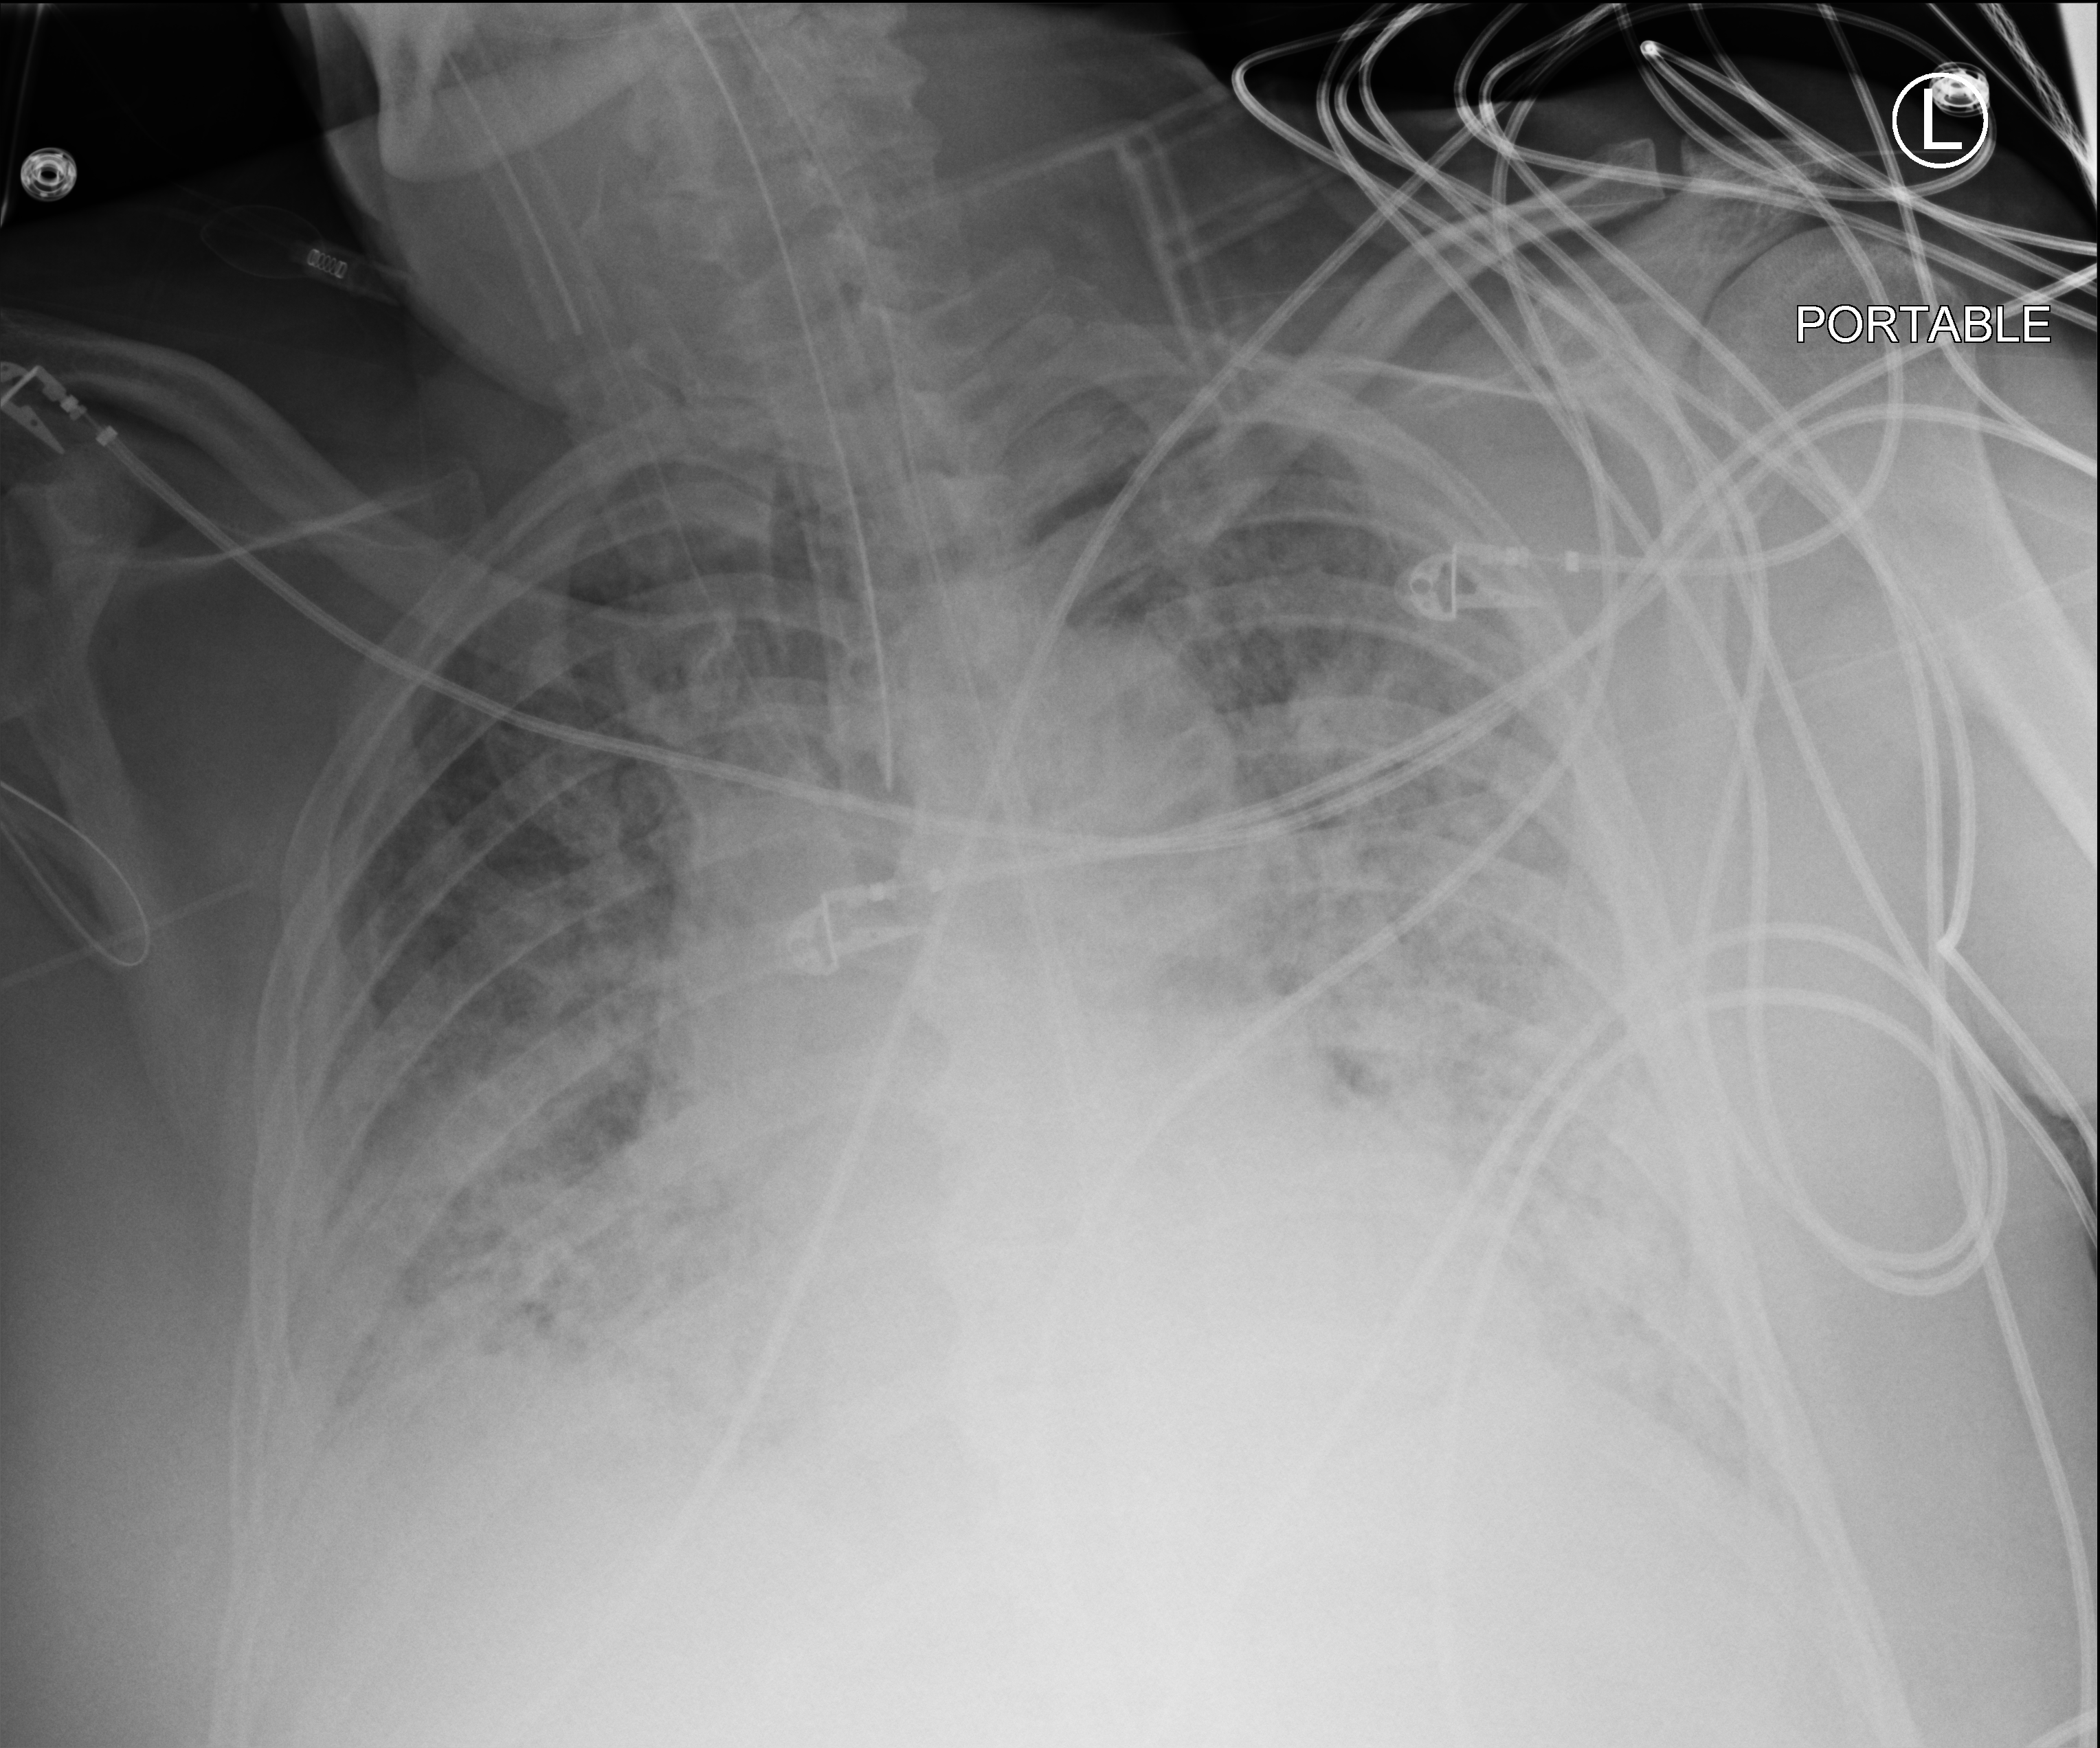
Portable chest radiograph. Patient hospitalised with COVID-19; male, aged 60–74 years.
Admission-level facts for this patient (not findings on this image; timing relative to this image not recorded): diabetes (admission record): no; hypertension (admission record): yes; other chronic lung disease (admission record): no.